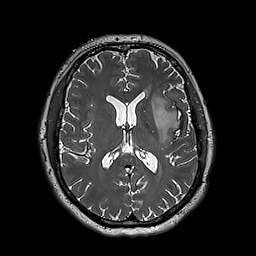
Brain MRI from a brain-tumour surgery series, one axial slice. Position 94 of 192 along the scan axis. 256 × 256 image matrix, field of view 250 × 250 mm. Case-level facts recorded for this patient, not image findings: histopathology: Astrocytoma; WHO grade: 3; IDH mutation: yes.
Structures marked on this image (outlined manually by an expert reader):
- tumour: bounding box (x1, y1, x2, y2) in pixels: (152, 94, 182, 144)